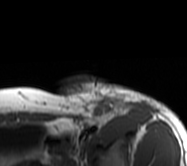
MRI of an extremity soft-tissue mass, one axial slice; slice 47 of 62 in the series (ordered by position); MR volume resampled by the dataset authors to the PET/CT grid (not the native acquisition matrix); 187 × 166 image matrix. Female patient. Case-level facts recorded for this patient, not image findings: histological type: leiomyosarcoma; grade: high; site of the primary tumour: groin.
Outlined on this slice (expert contour drawn on MRI and transferred to this co-registered scan by the dataset authors):
- gross tumour volume including surrounding oedema: box from (x=57, y=76) to (x=163, y=118) px
- gross tumour volume (mass): (x=66, y=81)–(x=110, y=118)